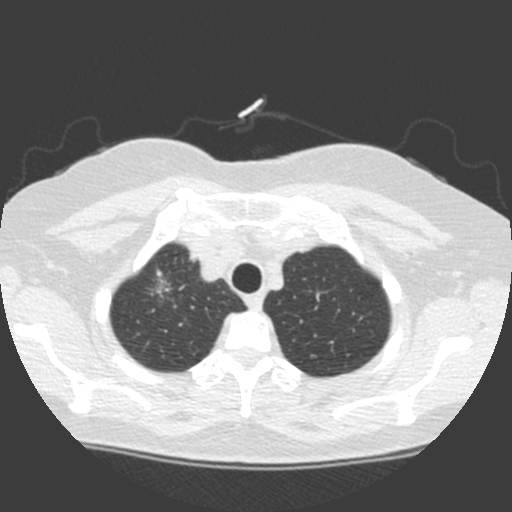
Low-dose screening chest CT, axial slice. Baseline annual screen. Lung window (W 1500 / L -600 HU). 2 mm slice thickness. Standard (soft-tissue) reconstruction kernel (C). Slice 18 of 155 in the series. 512 × 512 image matrix. Female, age 63 years at enrolment. Current smoker at enrolment.
• Expert reader's lesion annotation, box from (x=132, y=263) to (x=184, y=308) px.
• The exam's reader record, not a measurement of the box and not confirmed to be the same lesion: non-calcified nodule or mass ≥4 mm, right upper lobe, 11 × 11 mm, spiculated (stellate) margins, soft tissue attenuation.
• Official screen result: positive, change unspecified: nodule(s) >= 4 mm or enlarging nodule(s), mass(es), or other non-specific abnormalities suspicious for lung cancer.
• Lung cancer was diagnosed 6 days after this screen: adenocarcinoma, NOS, right upper lobe, poorly differentiated (G3), stage IA (AJCC 6th edition), 17 mm at pathology.